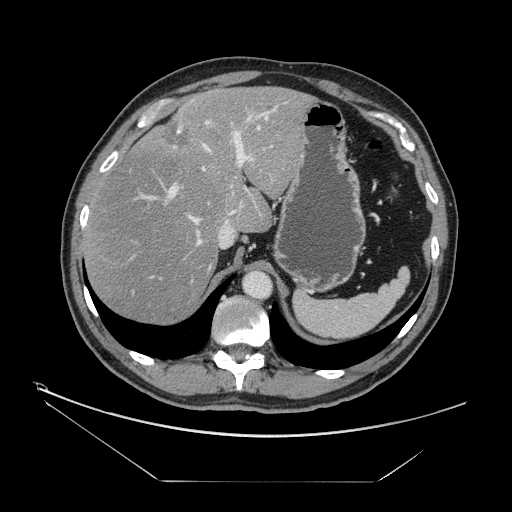
Contrast-enhanced abdominal CT, one axial slice. Intravenous contrast given. Soft-tissue window (W 400 / L 40 HU). 2.5 mm slice thickness. 512 × 512 image matrix, field of view 440 × 440 mm. Male patient, age 65 years. From the clinical record (not read from this slice): diagnosis: colorectal cancer liver metastases, imaged before liver resection; multiple liver metastases: yes; largest metastasis: 4.2 cm; disease in both lobes: yes.
Structures marked on this image (outlined manually by an expert reader):
- hepatic veins: bounding box (x1, y1, x2, y2) in pixels: (190, 112, 268, 248)
- liver: (84, 87, 311, 325)
- planned liver remnant (the part of the liver to remain after resection): (84, 87, 311, 325)
- portal vein (with intrahepatic branches): (136, 101, 289, 214)
- liver metastasis: (161, 122, 191, 149)